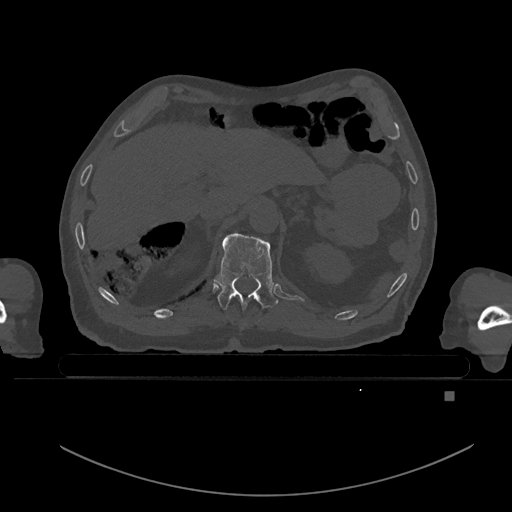
CT including the spine, one axial slice. Position 36 of 969 along the scan axis. Bone window (W 1800 / L 400 HU). 0.5 mm slice thickness. 512 × 512 image matrix. Male patient, age 82 years. Case-level facts recorded for this patient, not image findings: primary cancer: prostate; vertebrae with lytic lesions (as recorded): T11, T9, T8, T2.
Outlined on this slice (semi-automatic segmentation, software-assisted and operator-edited):
- T10 vertebra: box from (x=243, y=324) to (x=246, y=326) px
- T11 vertebra: (x=214, y=232)–(x=278, y=310)